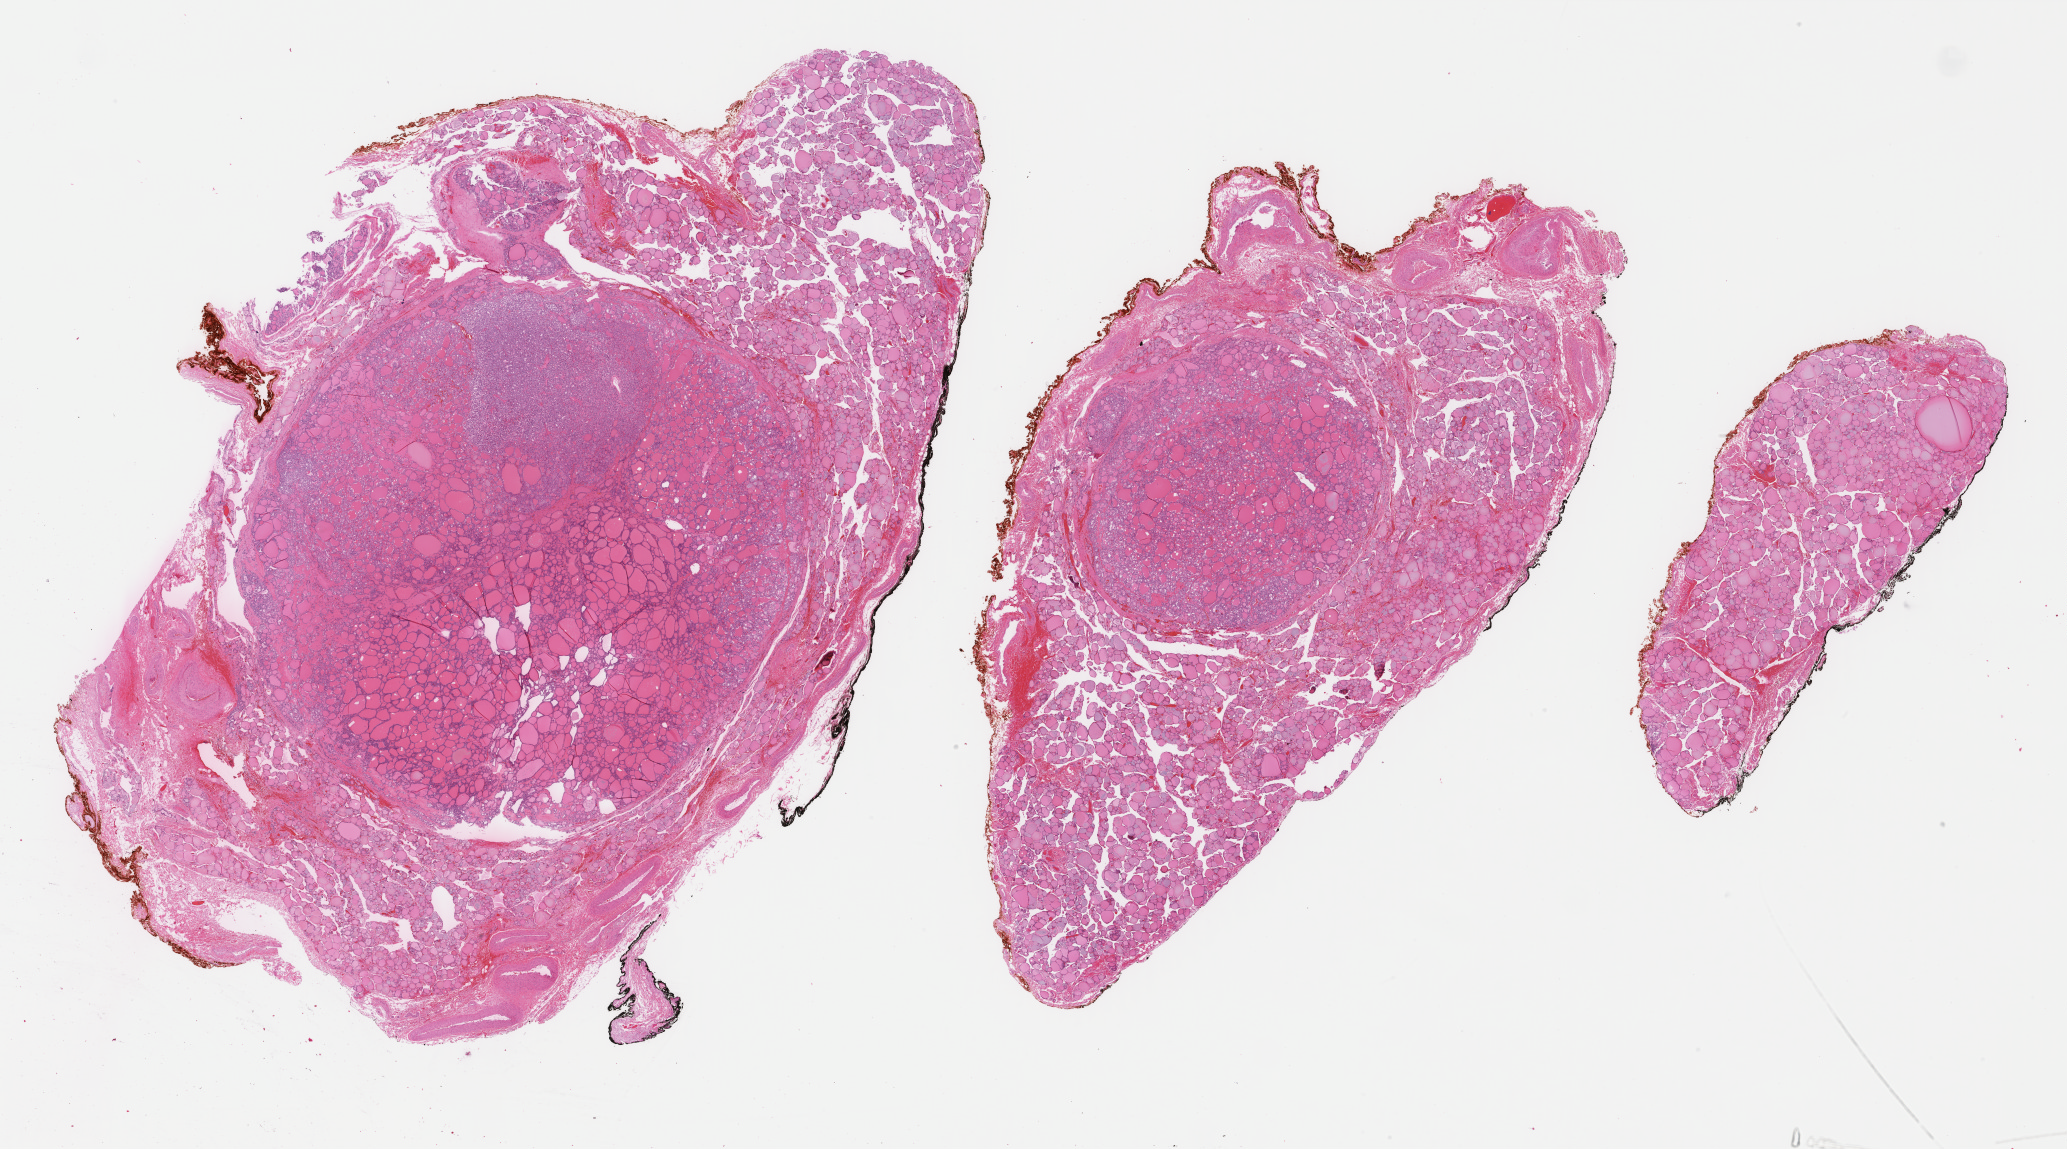
H&E whole-slide image, low-resolution overview of the scanned area, about 32.8 x 18.2 mm, FFPE section, sample: primary tumour, thyroid. Female patient; age at initial diagnosis 83 years.
* histologic diagnosis: Papillary carcinoma, follicular variant (thyroid gland)
* laterality: right
* AJCC pathologic stage: I